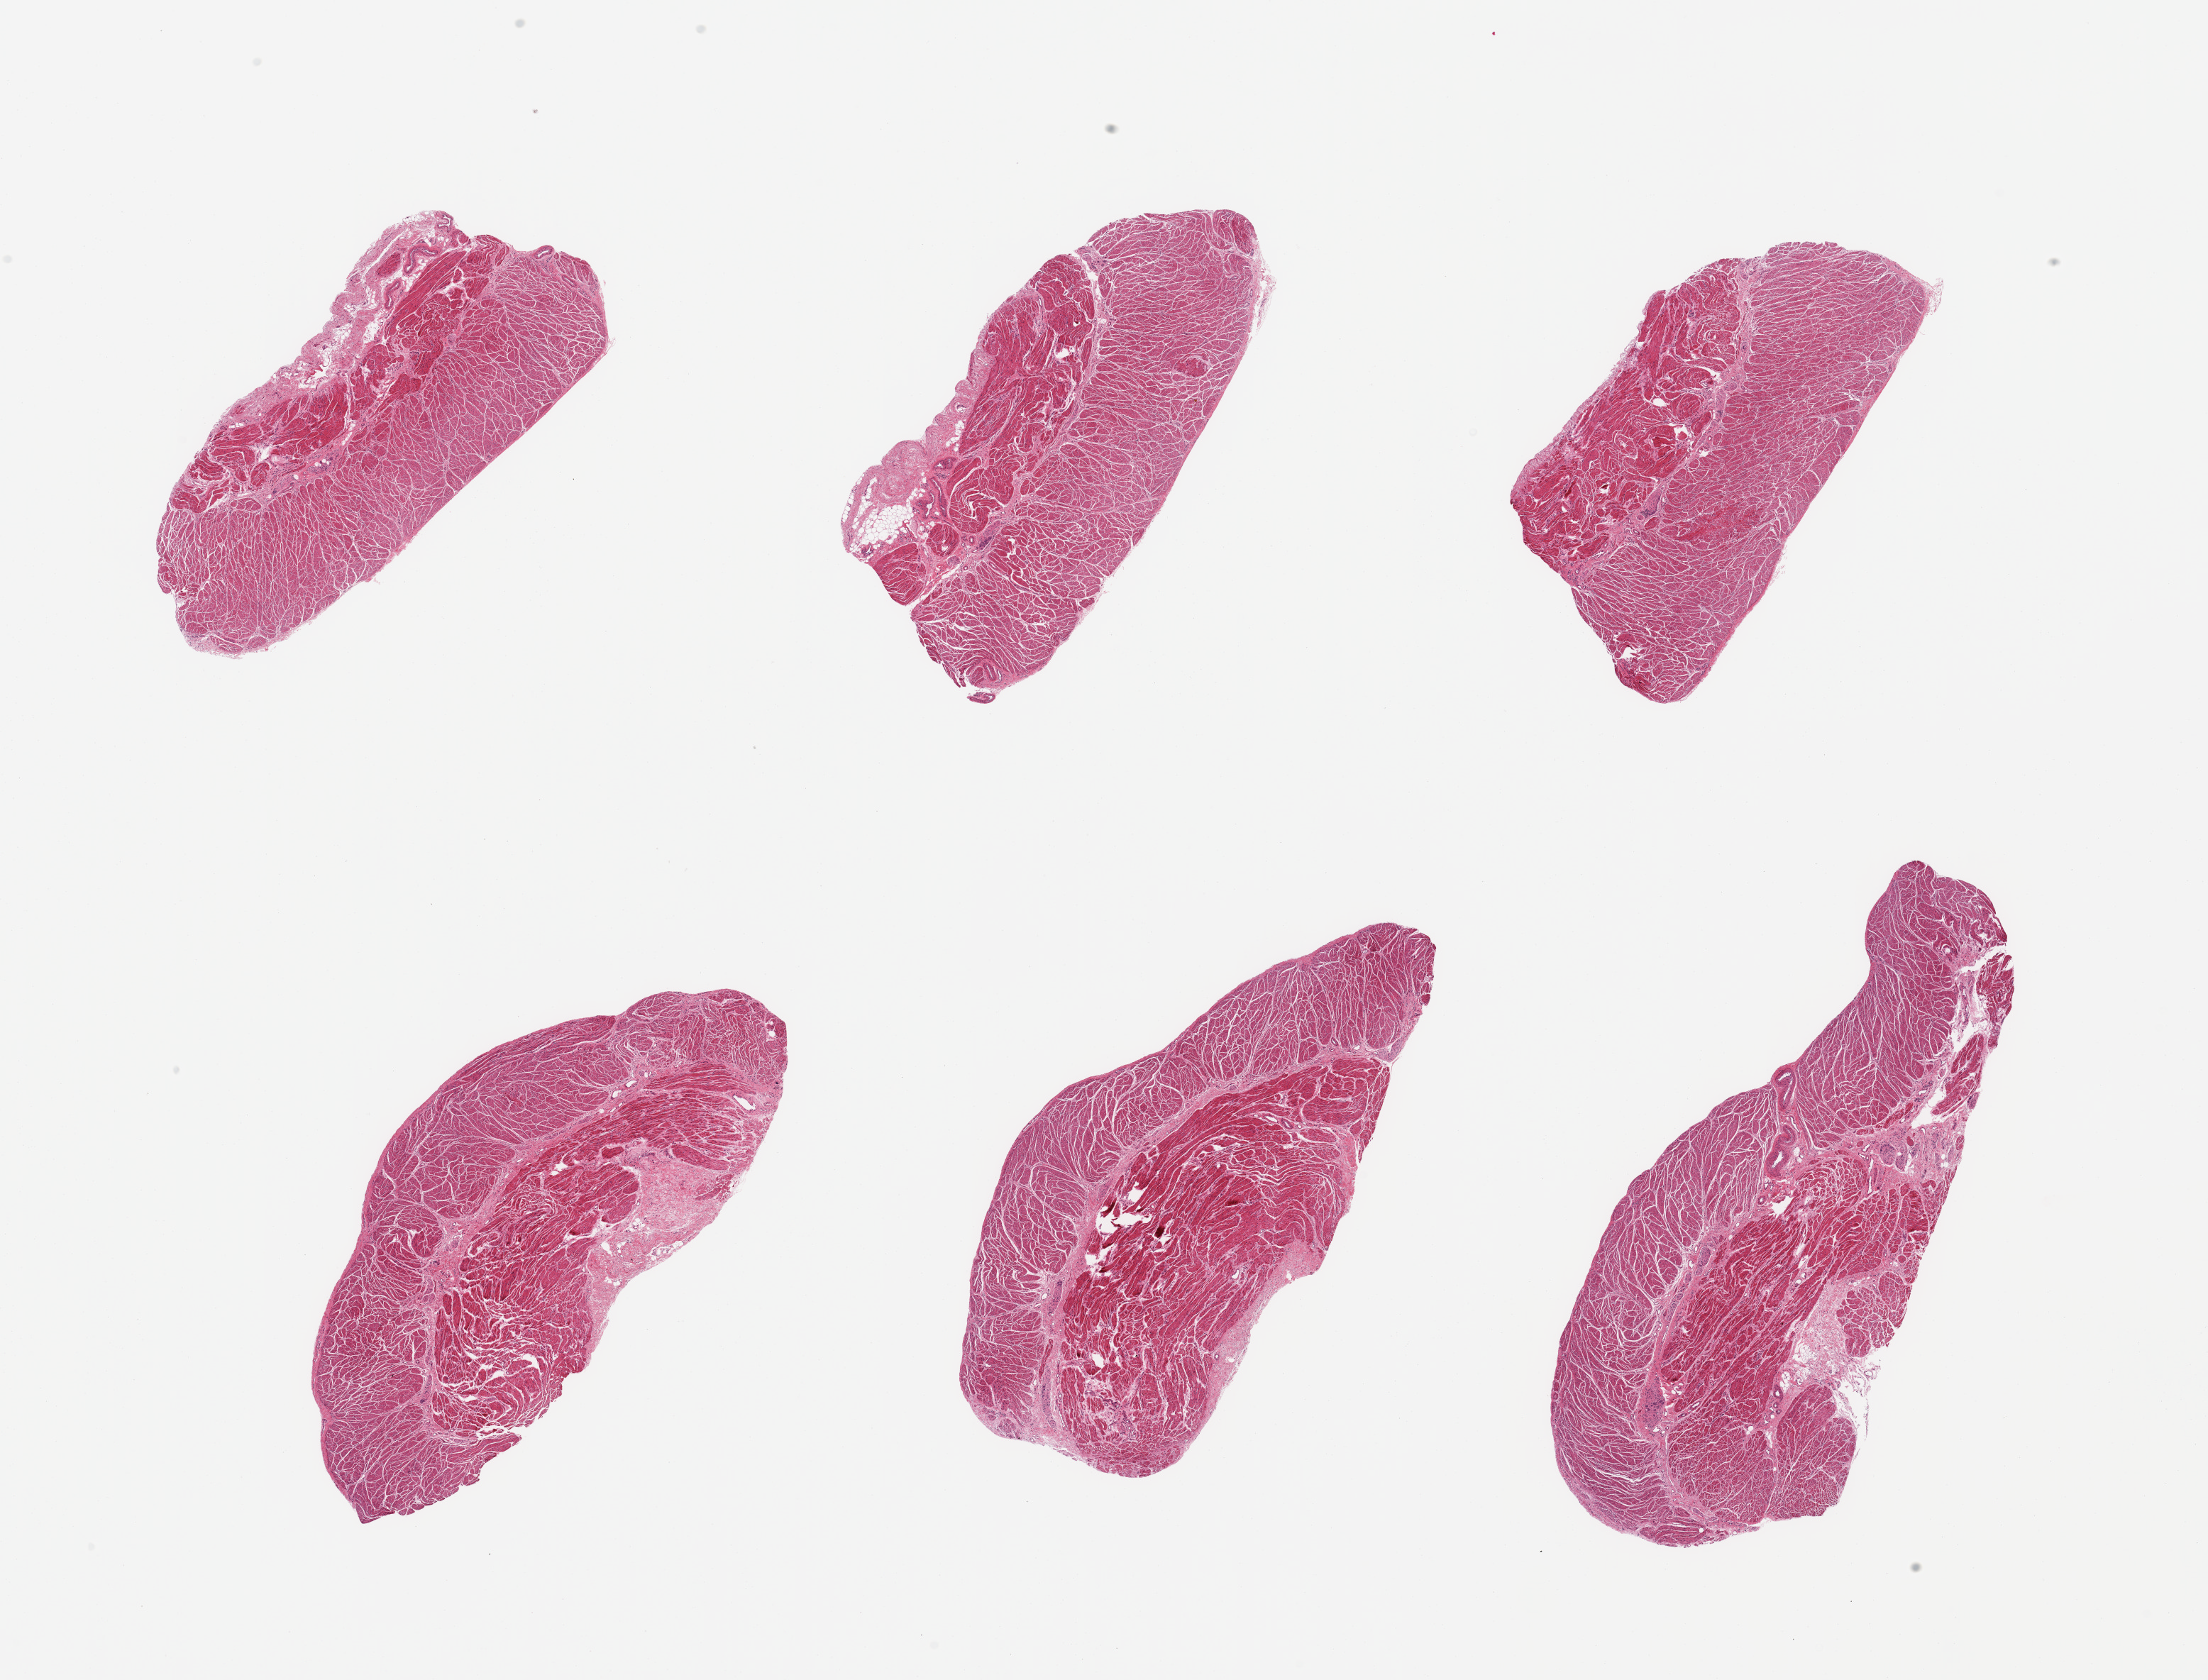
Hematoxylin and eosin (H&E) whole-slide image, a low-resolution overview of the entire scanned area, about 24.6 x 18.7 mm (slide scanned at 20x); PAXgene-fixed, paraffin-embedded tissue; section of gastroesophageal junction (target tissue); tissue donor sample. Male donor.
* review note (as recorded): 6 pieces; essentially well trimmed target muscularis